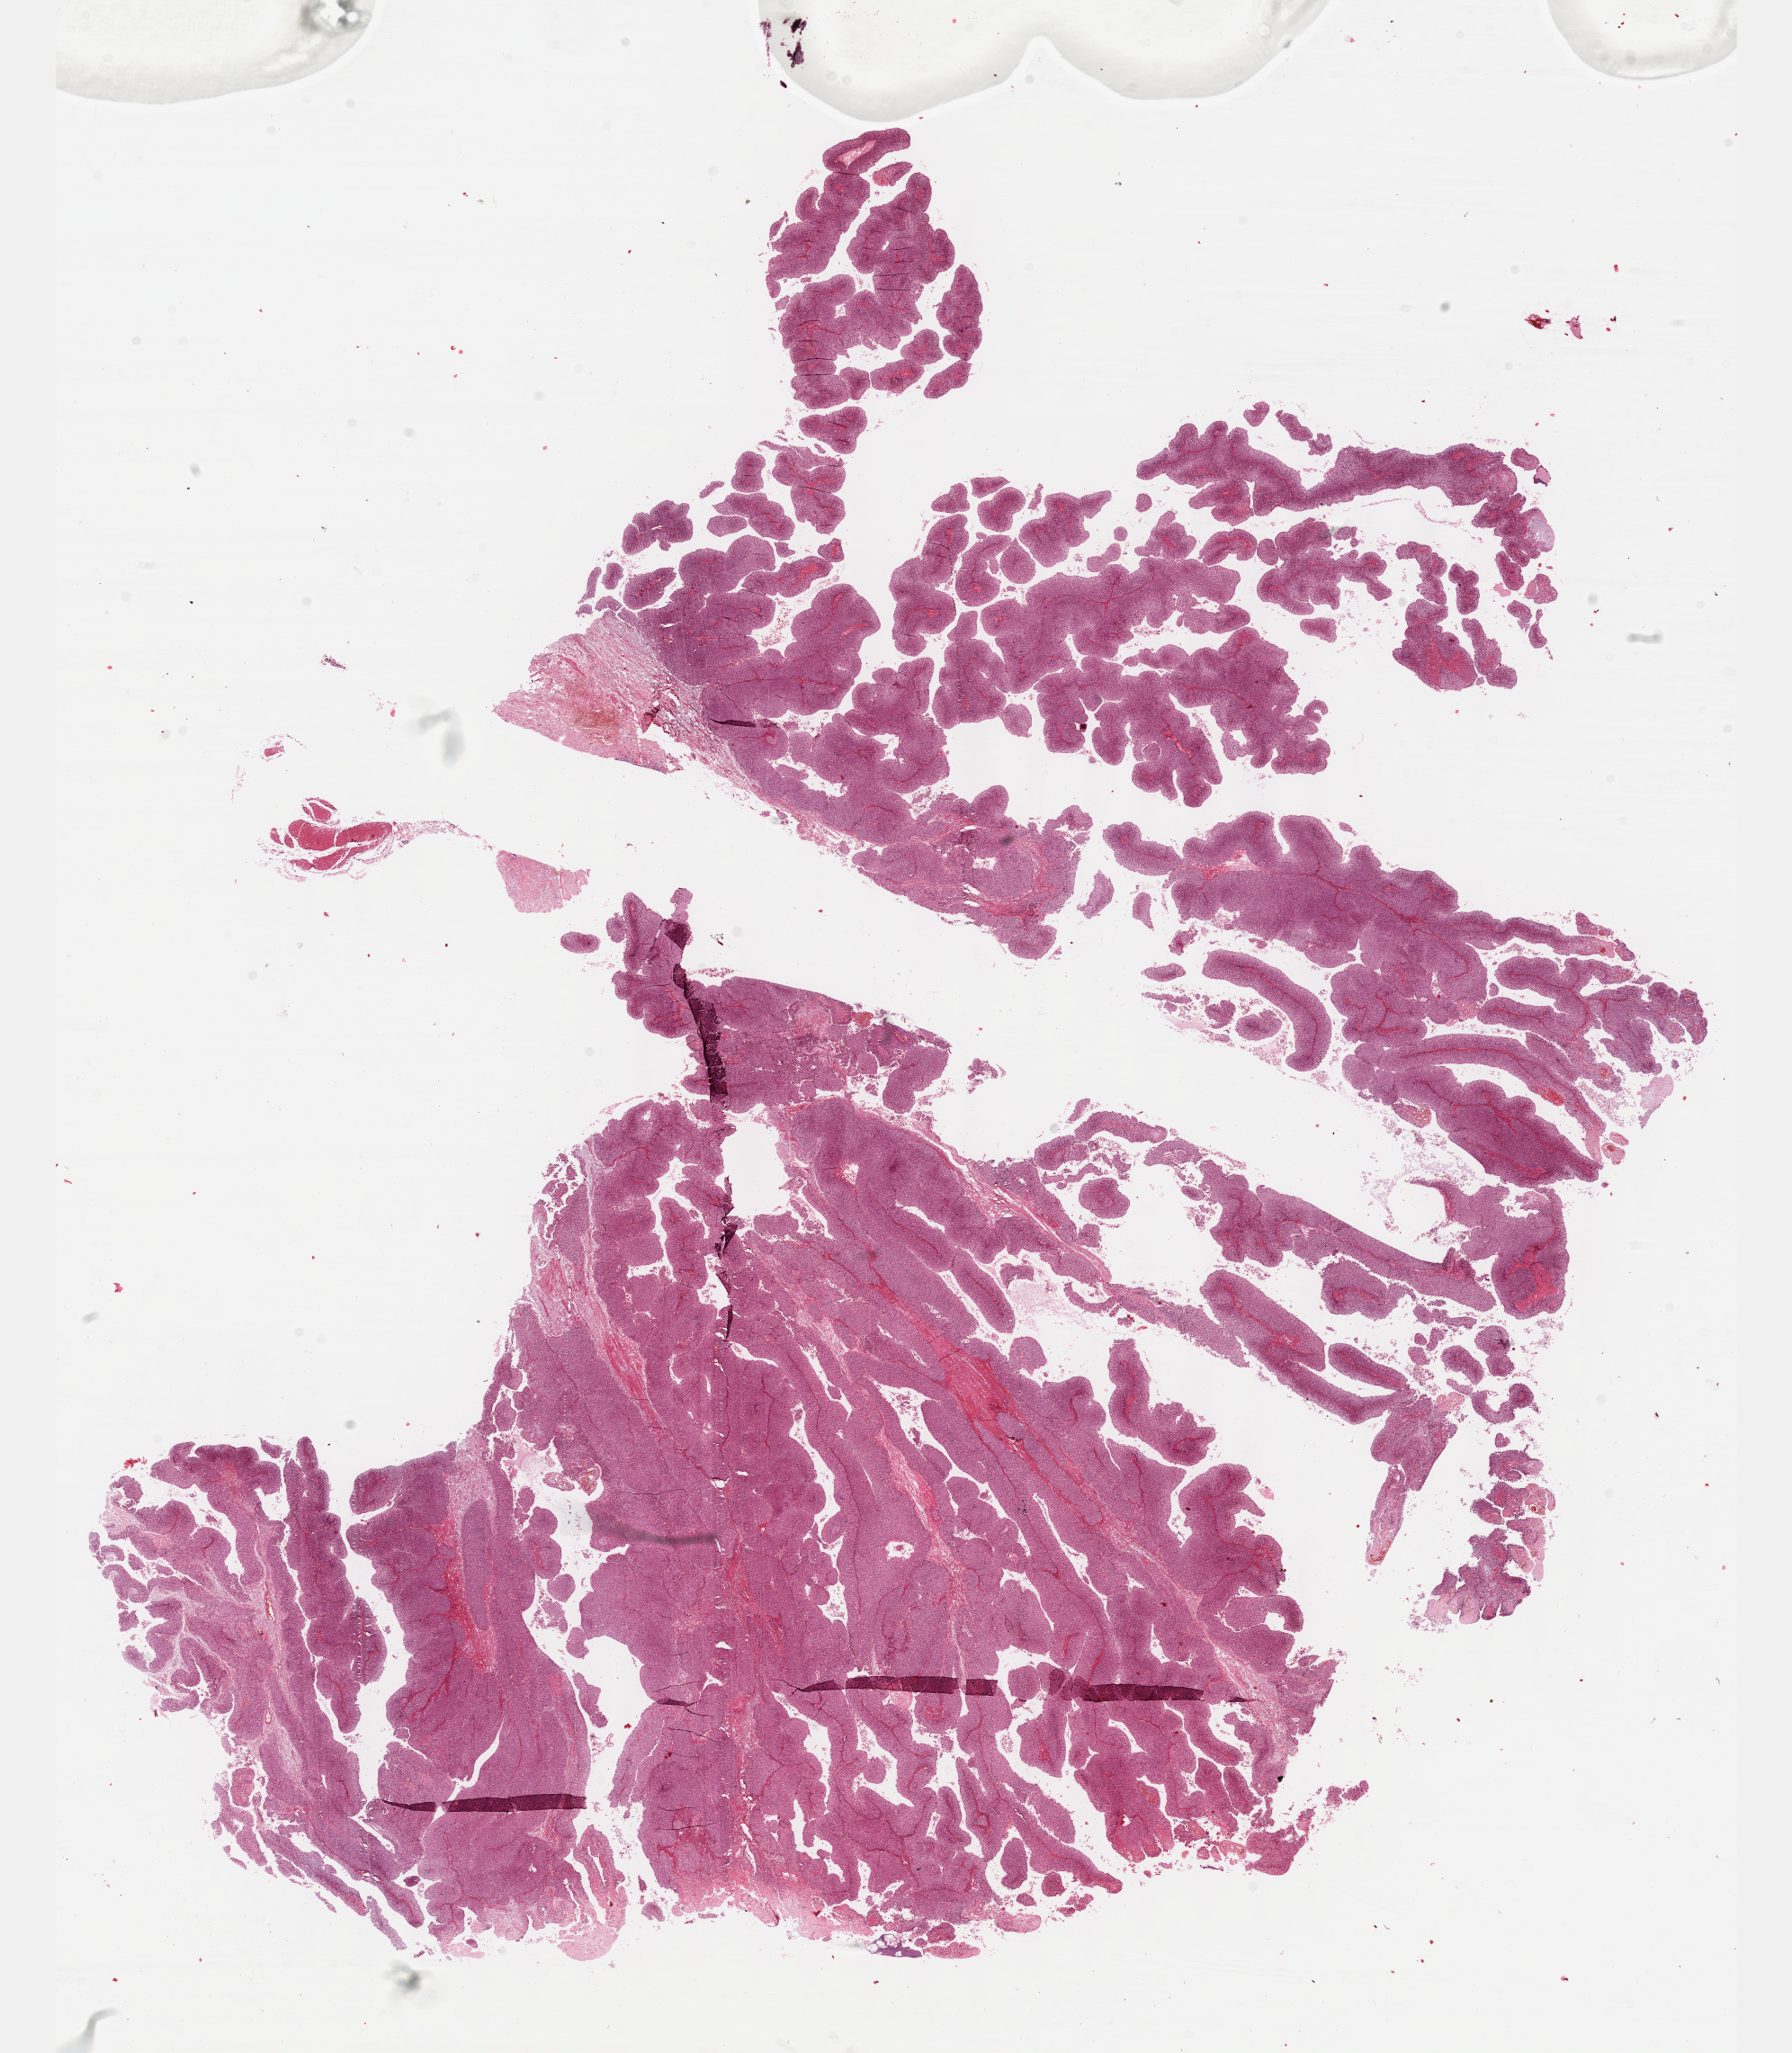
H&E whole-slide image — low-resolution overview of the scanned area, about 16.1 x 18.4 mm, formalin-fixed paraffin-embedded (FFPE) diagnostic section, sample: primary tumour, bladder. Female patient; age at initial diagnosis 55 years. Histologic grade: high grade.
- pathologic diagnosis: Transitional cell carcinoma
- AJCC pathologic stage: II (6th edition)